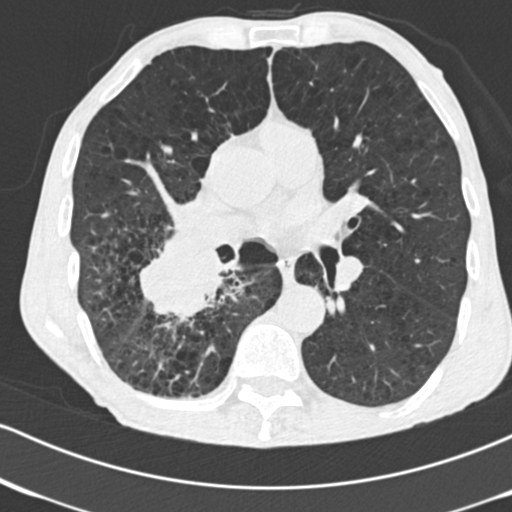
Low-dose screening chest CT, one axial slice; reconstruction kernel B30f; lung window (W 1500 / L -600 HU); 2 mm slice thickness; 512 × 512 image matrix.
Annotated regions visible in this slice (outlined manually by an expert reader):
- lesion 1 (tumor, lower lobe of right lung): bounding box [x1, y1, x2, y2] px = [140, 233, 224, 318]